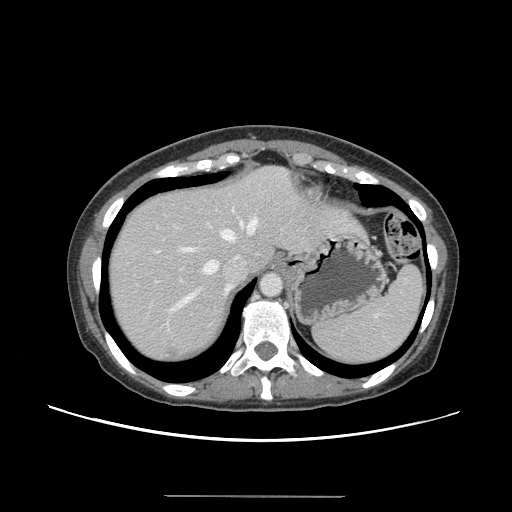
Contrast-enhanced abdominal CT, one axial slice. Slice 118 of 144 in the series (ordered by position). Intravenous contrast given. Soft-tissue window (W 400 / L 40 HU). 2.5 mm slice thickness. 512 × 512 image matrix. Female patient, age 53 years. From the clinical record (not read from this slice): diagnosis: colorectal cancer liver metastases, imaged before liver resection; multiple liver metastases: yes.
Outlined on this slice (expert manual segmentation):
- hepatic veins: bounding box [x1, y1, x2, y2] px = [174, 217, 258, 309]
- liver: [109, 167, 364, 363]
- planned liver remnant (the part of the liver to remain after resection): [108, 167, 287, 298]
- portal vein (with intrahepatic branches): [155, 281, 158, 283]
- liver metastasis: [165, 348, 178, 360]